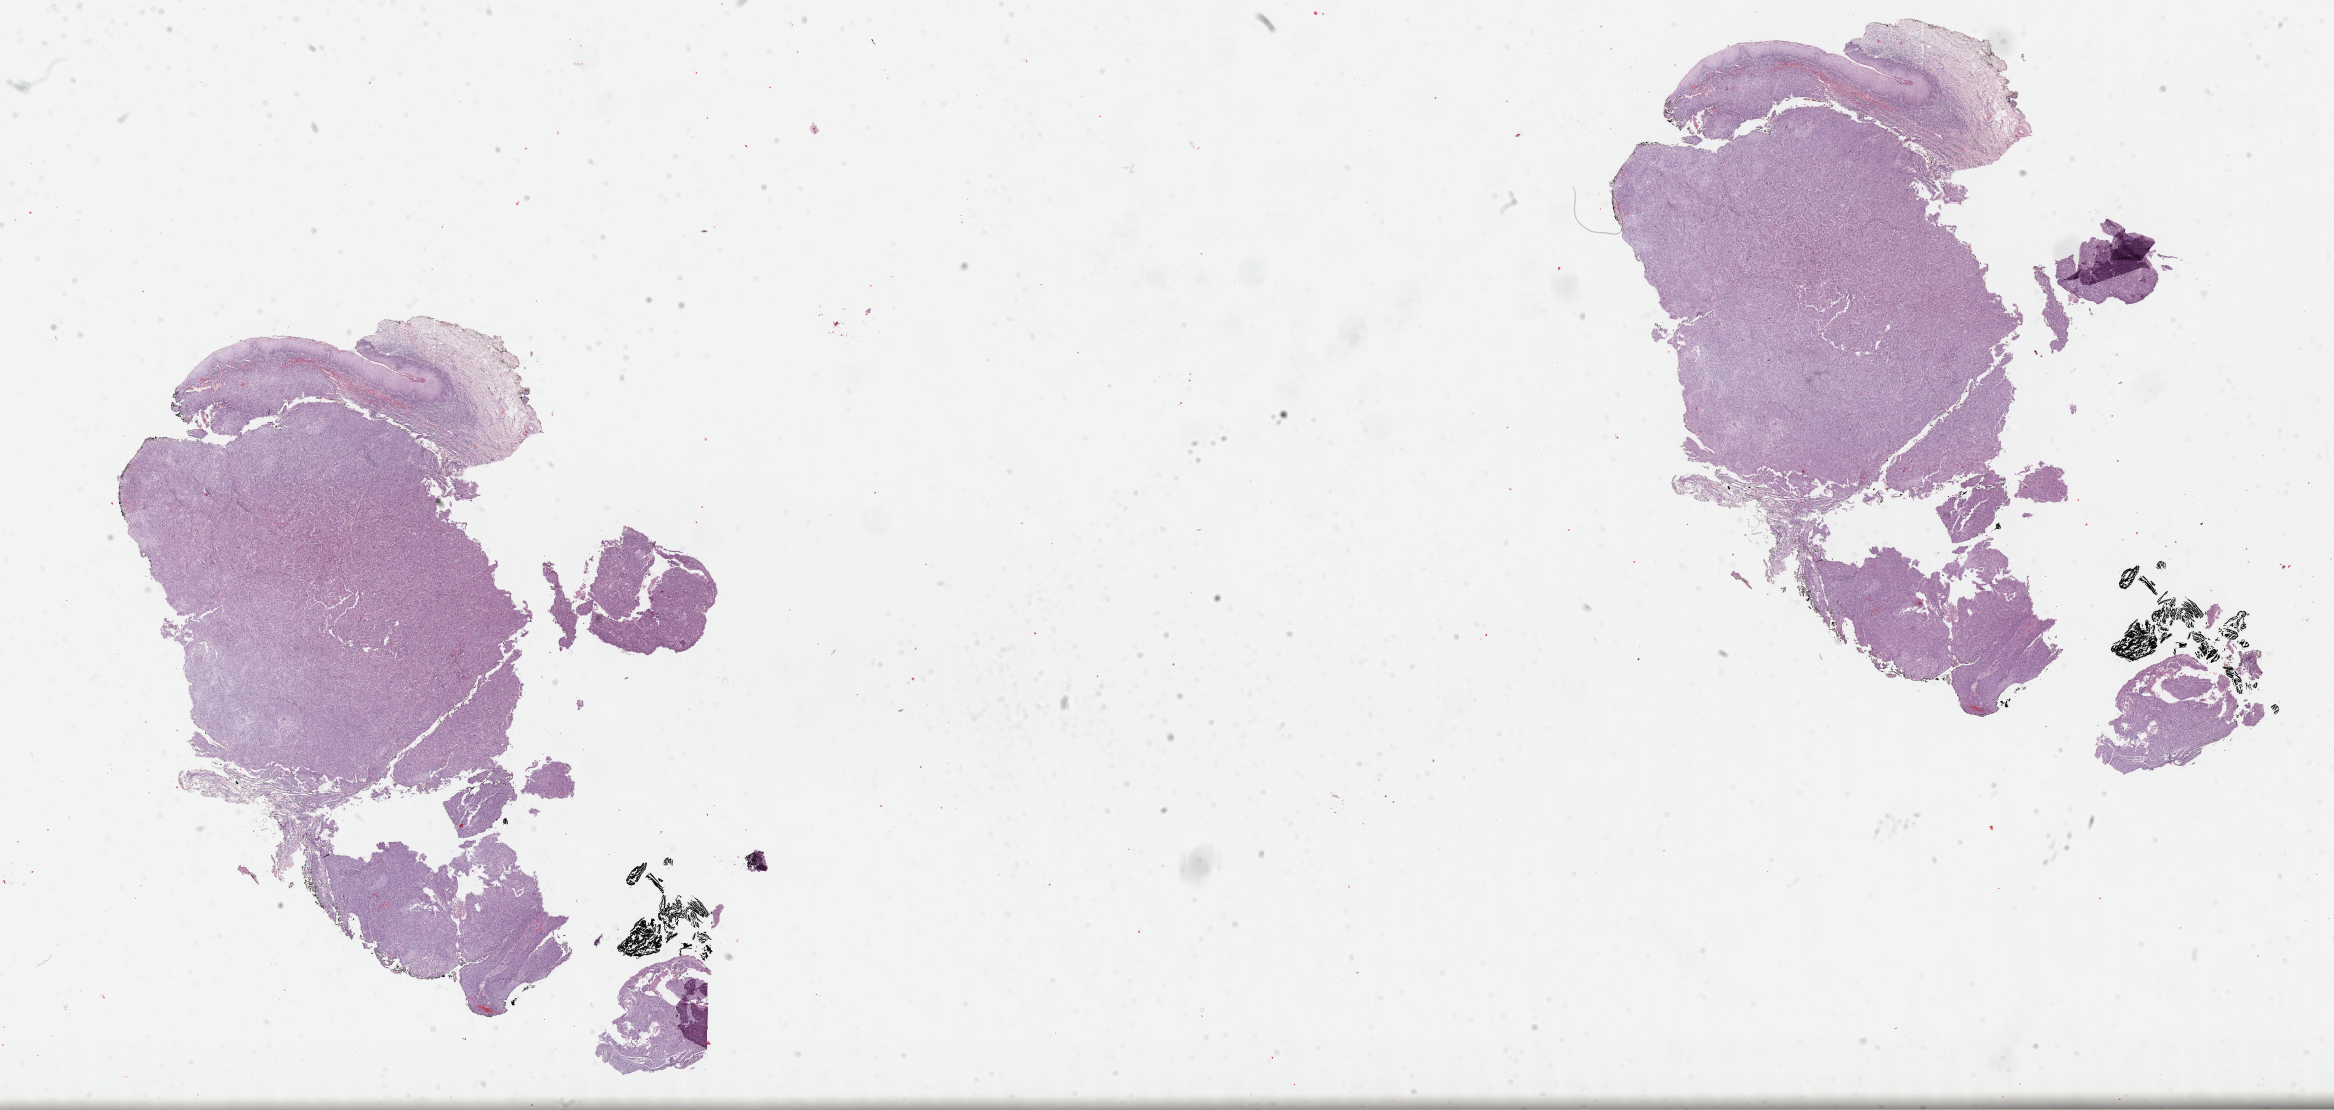
Whole-slide histology image, Hematoxylin and eosin (H&E) stained — whole scanned area (about 37.8 x 18.0 mm) shown as a low-resolution overview. FFPE section. Primary tumour sample from the head and neck. Male, age 71 years at initial diagnosis. Histologic grade: G3 (poorly differentiated).
• laterality: left
• diagnosis: Squamous cell carcinoma, NOS (cheek mucosa)
• AJCC pathologic stage: III (7th edition)